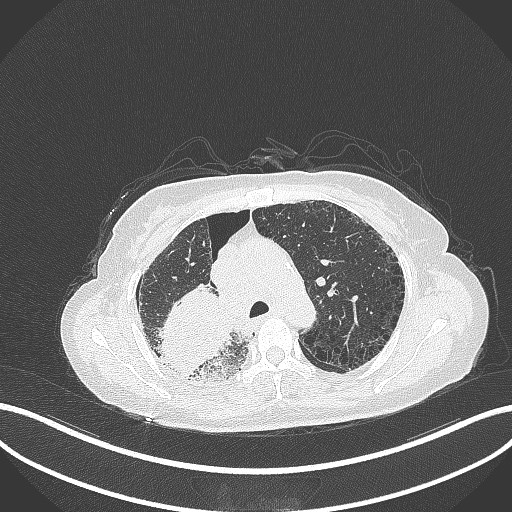
Chest CT, one axial slice; position 245 of 408 along the scan axis; reconstruction kernel B70f; 120 kVp; lung window (W 1500 / L -600 HU); 1 mm slice thickness; 512 × 512 image matrix. Patient: female, 64 years. Case-level facts recorded for this patient, not image findings: clinical TNM (as recorded): T3 N3 M0.
Outlined on this slice (bounding box drawn by a radiologist):
- lung tumour (recorded histology: squamous cell carcinoma): bounding box [x1, y1, x2, y2] px = [151, 281, 238, 379]